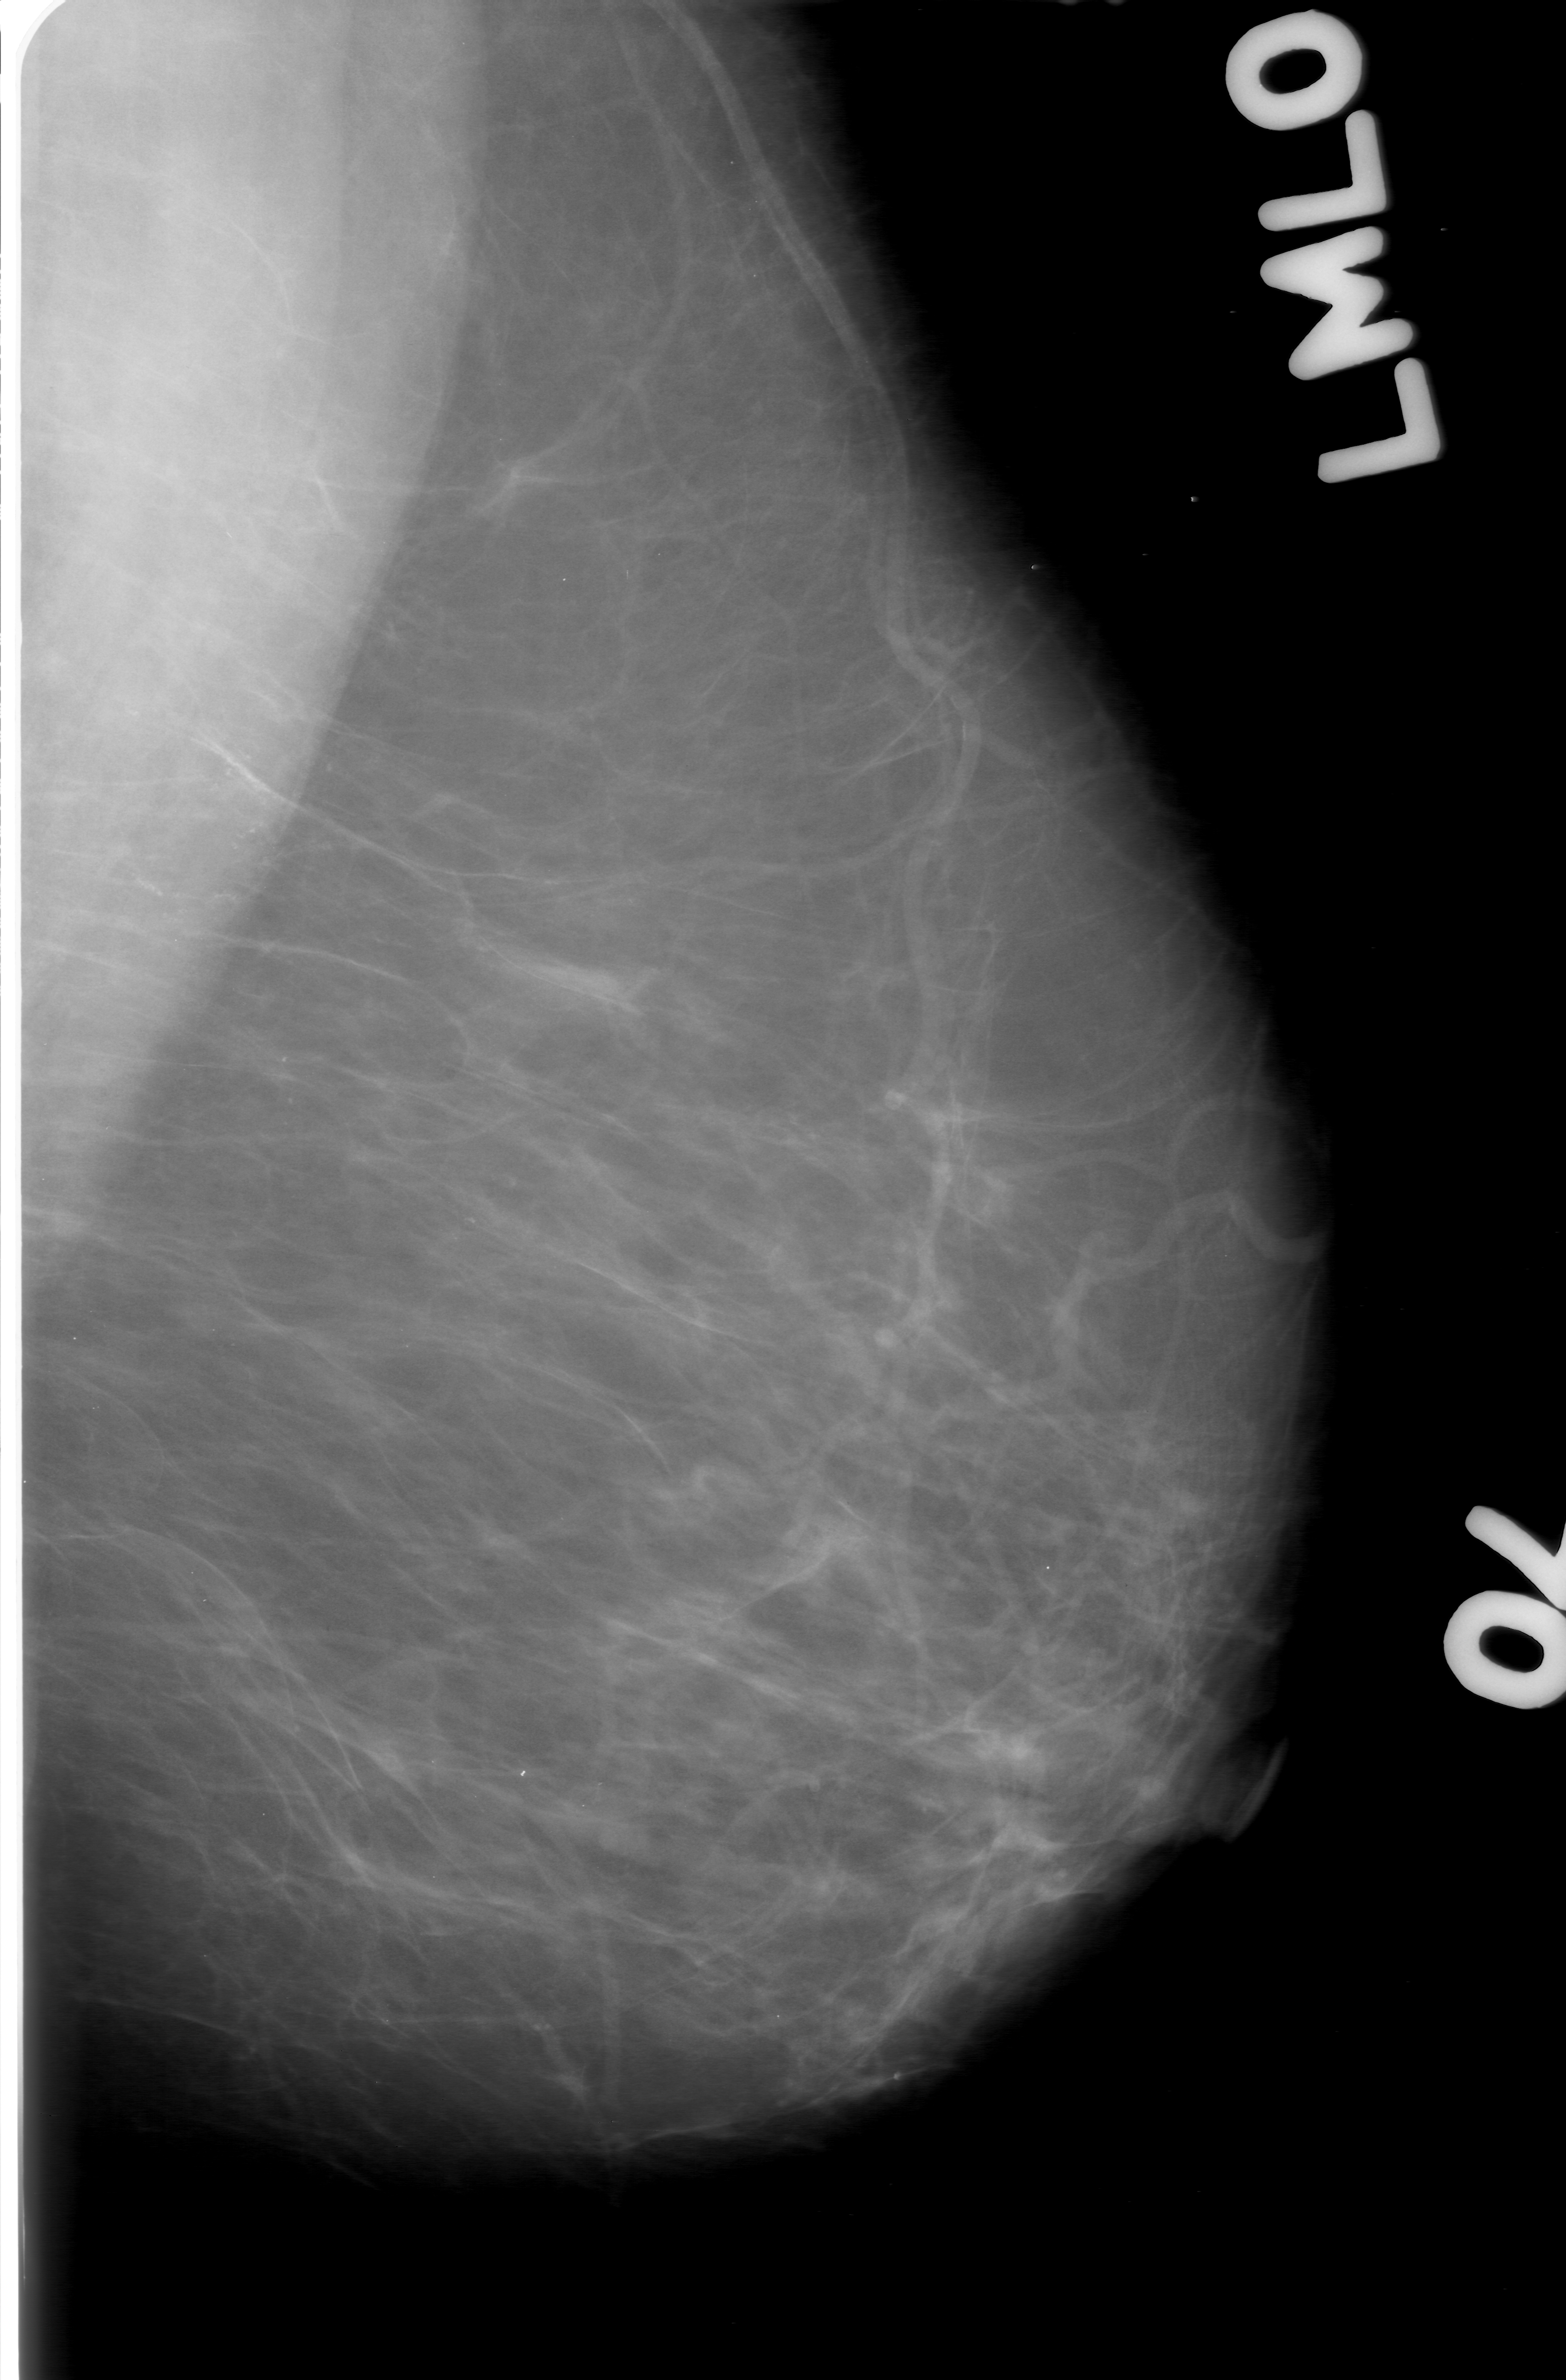
Scanned film-screen mammogram, left breast, mediolateral oblique (MLO) view.
Marked findings (only marked abnormalities are described; nothing is implied about the rest of the image): calcifications, morphology amorphous, distribution linear; BI-RADS assessment category 3; pathology (as recorded): malignant.